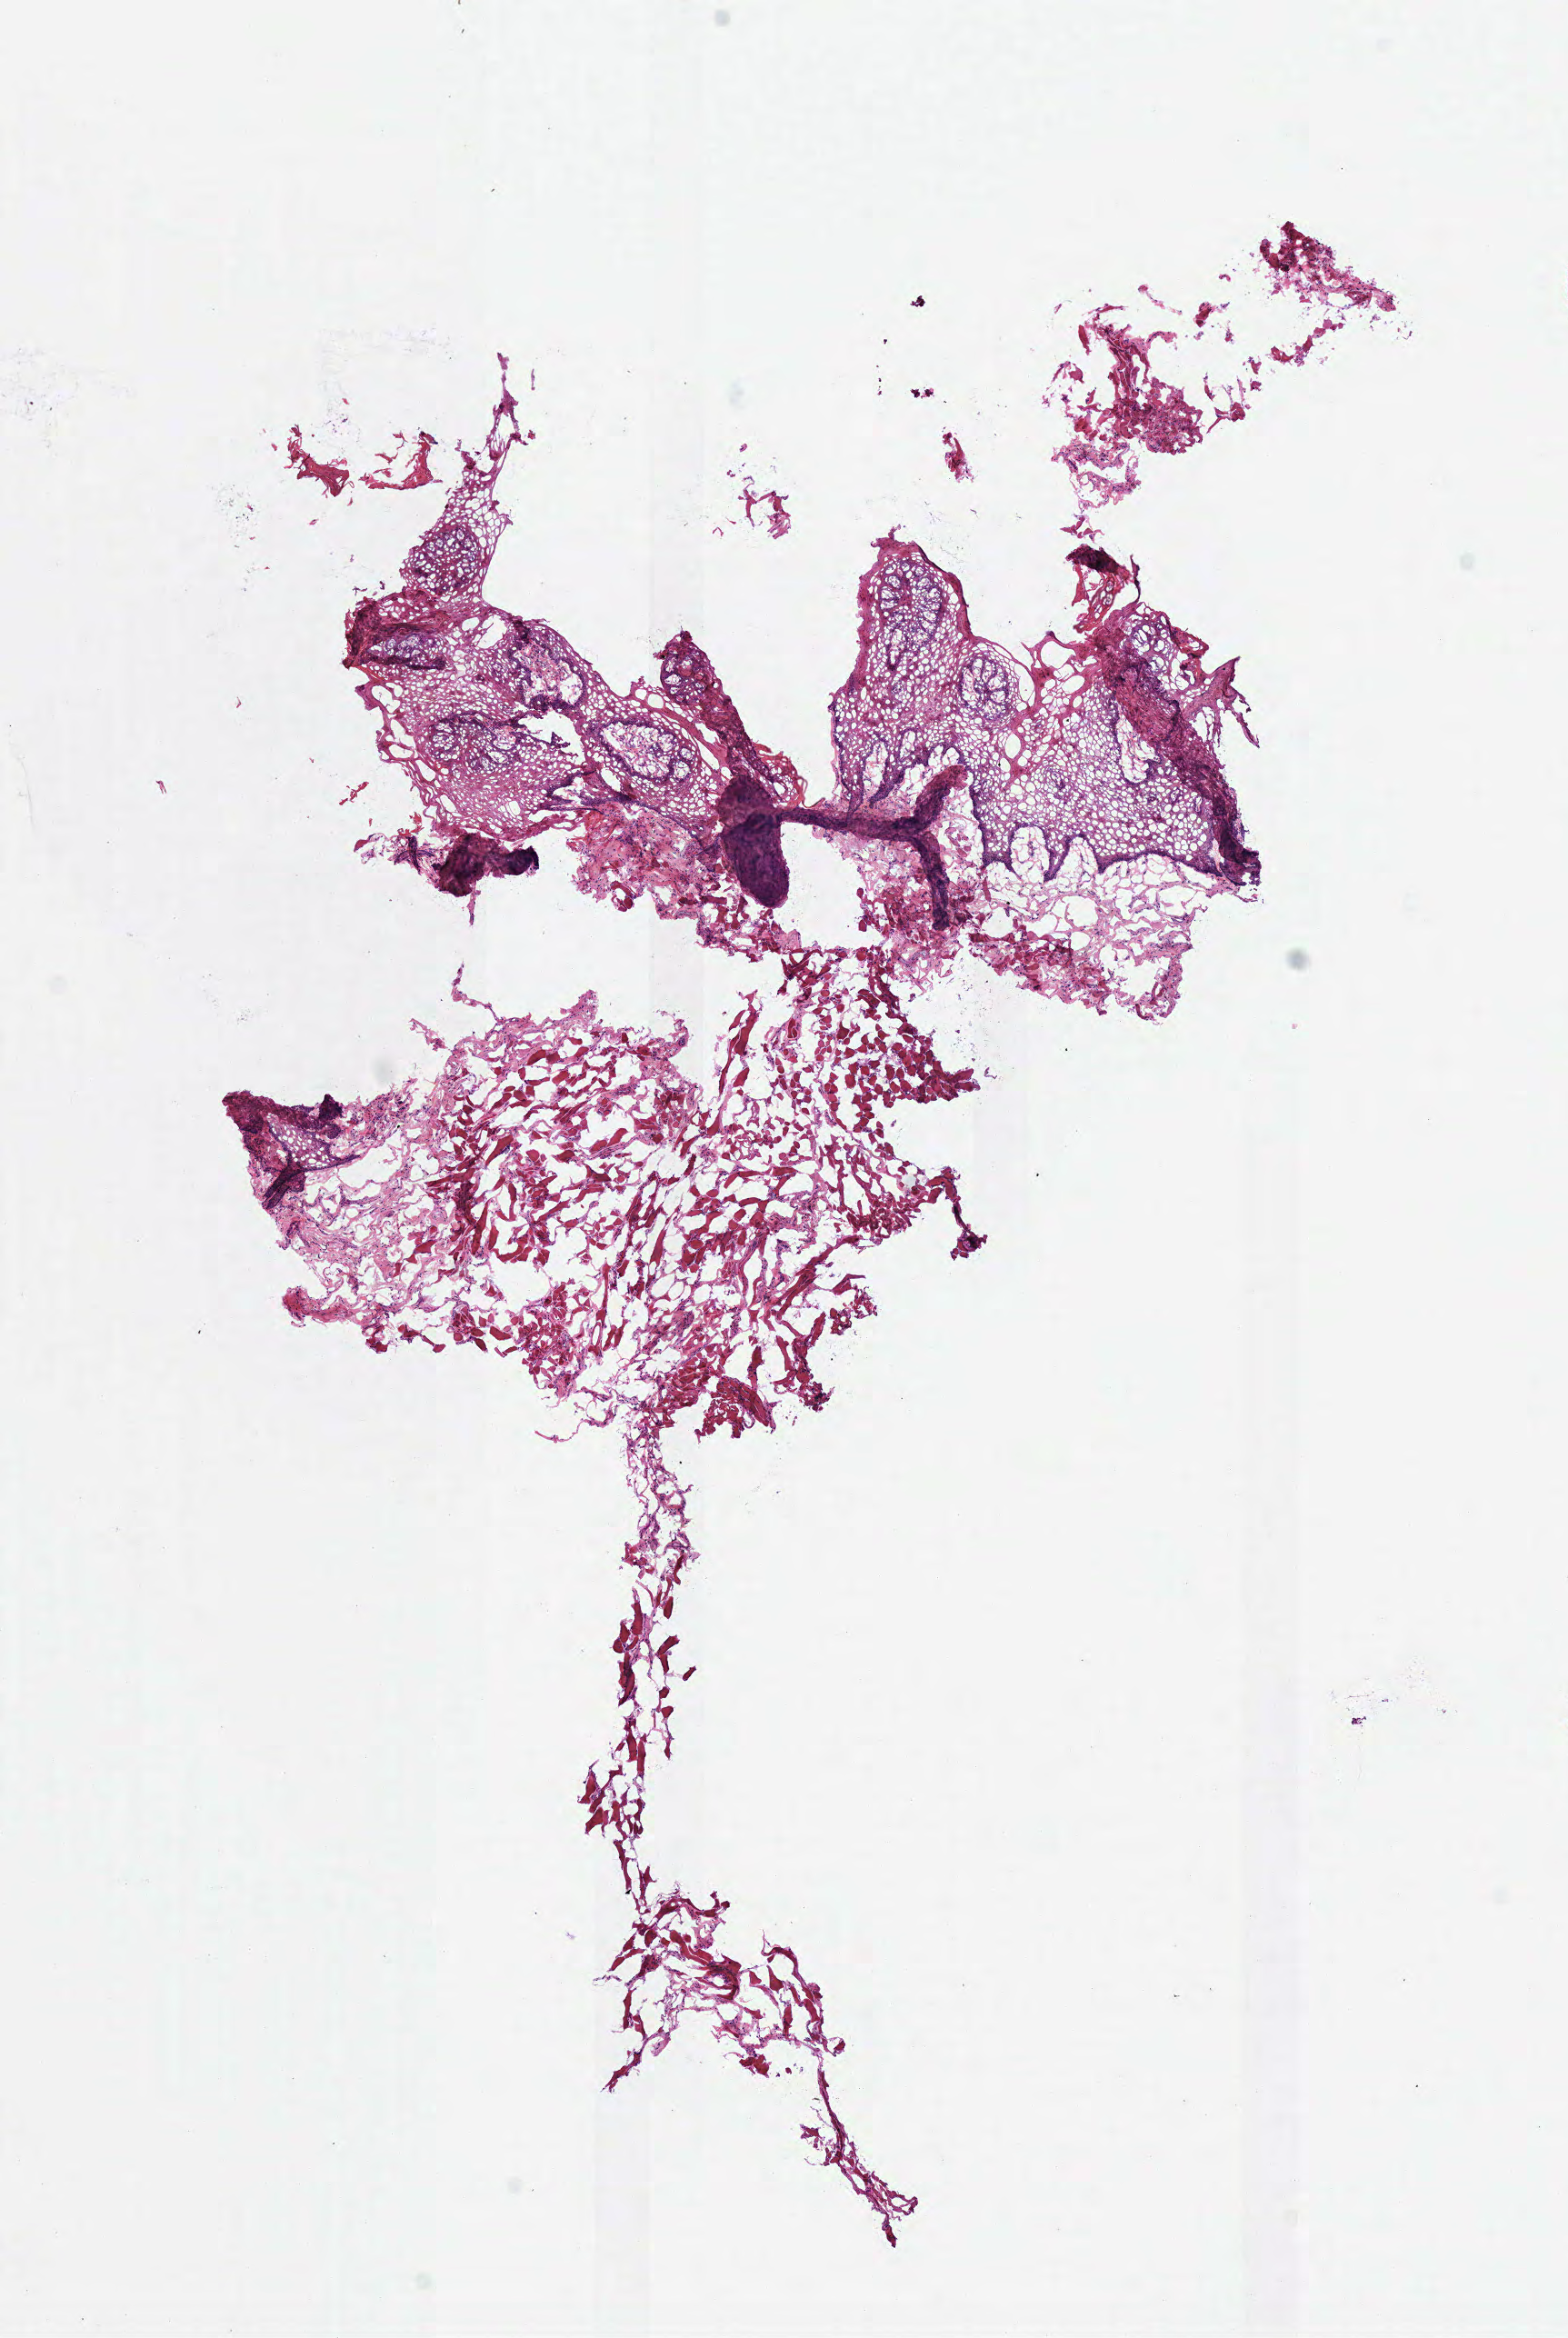
Digitized H&E-stained tissue section (whole slide) — a low-resolution overview of the entire scanned area, about 6.8 x 10.1 mm (from a 40x scan), frozen section from the top of the tissue portion, head and neck, solid tissue normal (non-tumour tissue) sample. Male patient; age at initial diagnosis 59 years.
- this section: solid tissue normal sample (biorepository sample class)
- patient diagnosis: Squamous cell carcinoma, NOS (tongue, NOS)